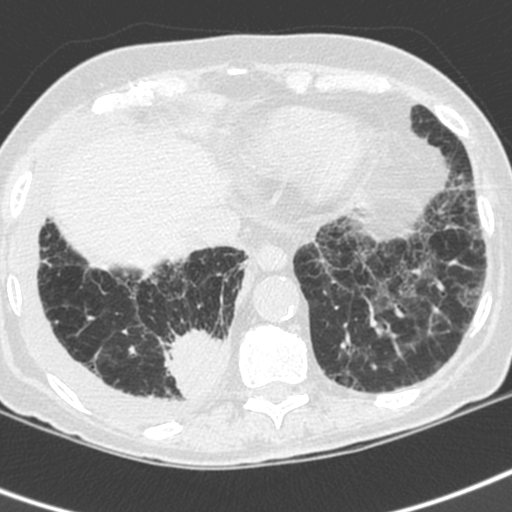
Chest CT (low-dose screening protocol), one axial image, baseline screening round, lung window (W 1500 / L -600 HU), slice 149 of 192 in the series. Female, age 73 years at enrolment. Current smoker at enrolment.
Expert reader's lesion annotation, bounding box [x1, y1, x2, y2] px = [159, 323, 235, 405]. Reader record for this screening exam (exam-level; its link to the box is not recorded): non-calcified nodule or mass ≥4 mm, right lower lobe, 35 × 30 mm, spiculated (stellate) margins, soft tissue attenuation. Official screen result: positive, change unspecified: nodule(s) >= 4 mm or enlarging nodule(s), mass(es), or other non-specific abnormalities suspicious for lung cancer.